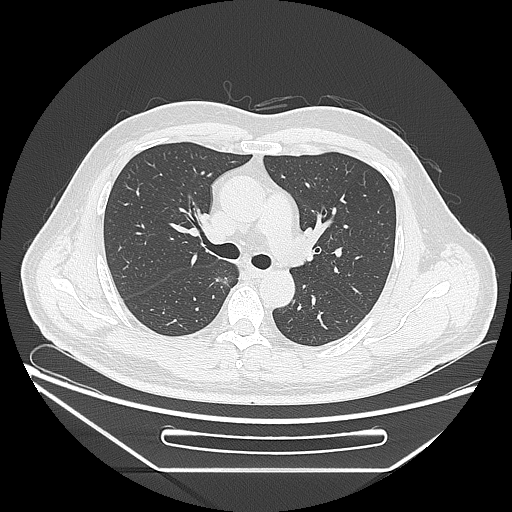
Chest CT, one axial slice. Slice 161 of 271 in the series (ordered by position). Reconstruction kernel LUNG. 120 kVp. Lung window (W 1500 / L -600 HU). 1.25 mm slice thickness. 512 × 512 image matrix. Male patient, age 49 years. Case-level facts recorded for this patient, not image findings: clinical TNM (as recorded): T1b N0 M0; histopathological grade: G2.
Structures marked on this image (bounding box drawn by a radiologist):
- lung tumour (recorded histology: adenocarcinoma): bounding box (x1, y1, x2, y2) in pixels: (211, 269, 230, 291)